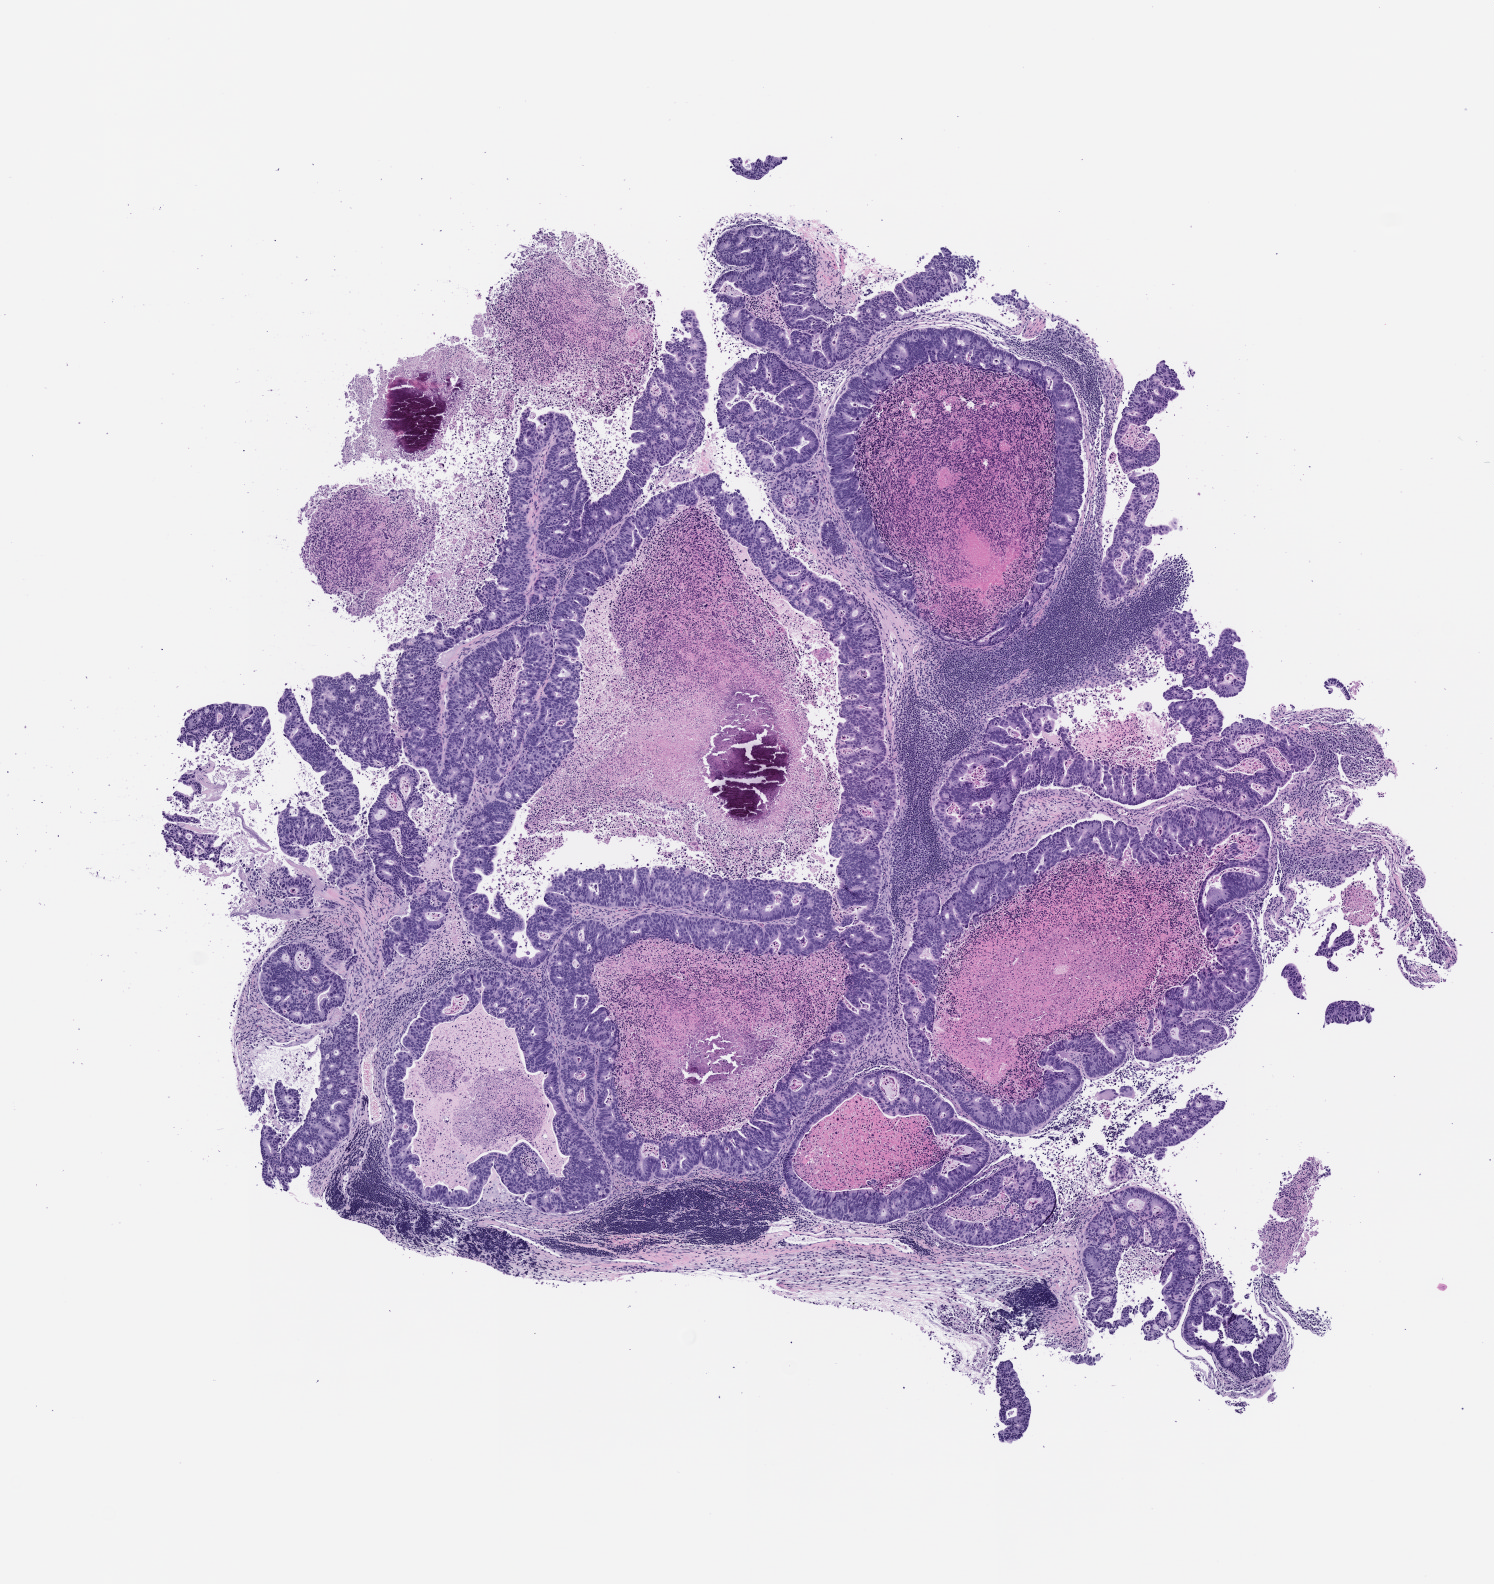
H&E whole-slide image of a patient-derived xenograft (PDX) tumor grown in a mouse, passage 1 — a low-resolution overview of the entire scanned area, about 6.0 x 6.4 mm, FFPE section, tumor site category: colon.
Originating patient diagnosis: Colon Adenocarcinoma.